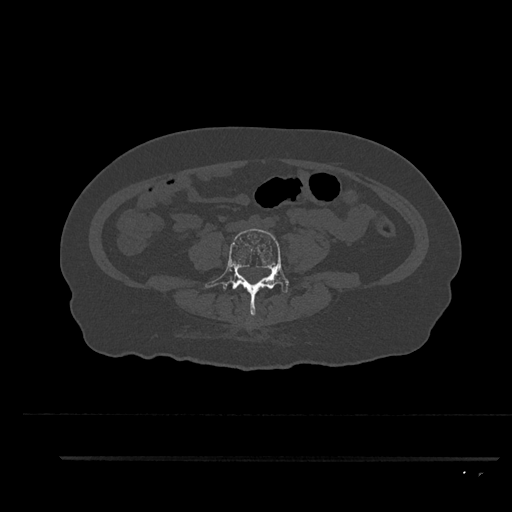
CT including the spine, one axial slice. Position 23 of 797 along the scan axis. 120 kVp. Bone window (W 1800 / L 400 HU). 0.5 mm slice thickness. 512 × 512 image matrix. Female patient, age 44 years. From the clinical record (not read from this slice): primary cancer: renal; vertebrae with lytic lesions (as recorded): L1.
Annotated regions visible in this slice (semi-automatic segmentation, software-assisted and operator-edited):
- L4 vertebra: bounding box <205,228,289,316> (left, top, right, bottom; pixels)